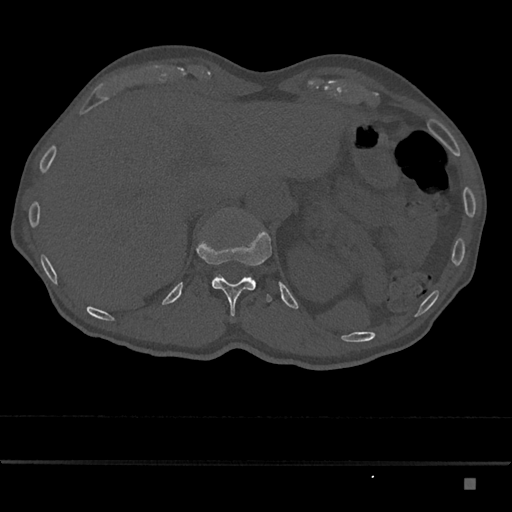
CT including the spine, one axial slice; position 603 of 797 along the scan axis; reconstruction kernel Br40s/3; bone window (W 1800 / L 400 HU); 512 × 512 image matrix, field of view 390 × 390 mm. Patient: male, 72 years. From the clinical record (not read from this slice): primary cancer: prostate.
Outlined on this slice (semi-automatic segmentation, software-assisted and operator-edited):
- T12 vertebra: bounding box <196,232,272,317> (left, top, right, bottom; pixels)